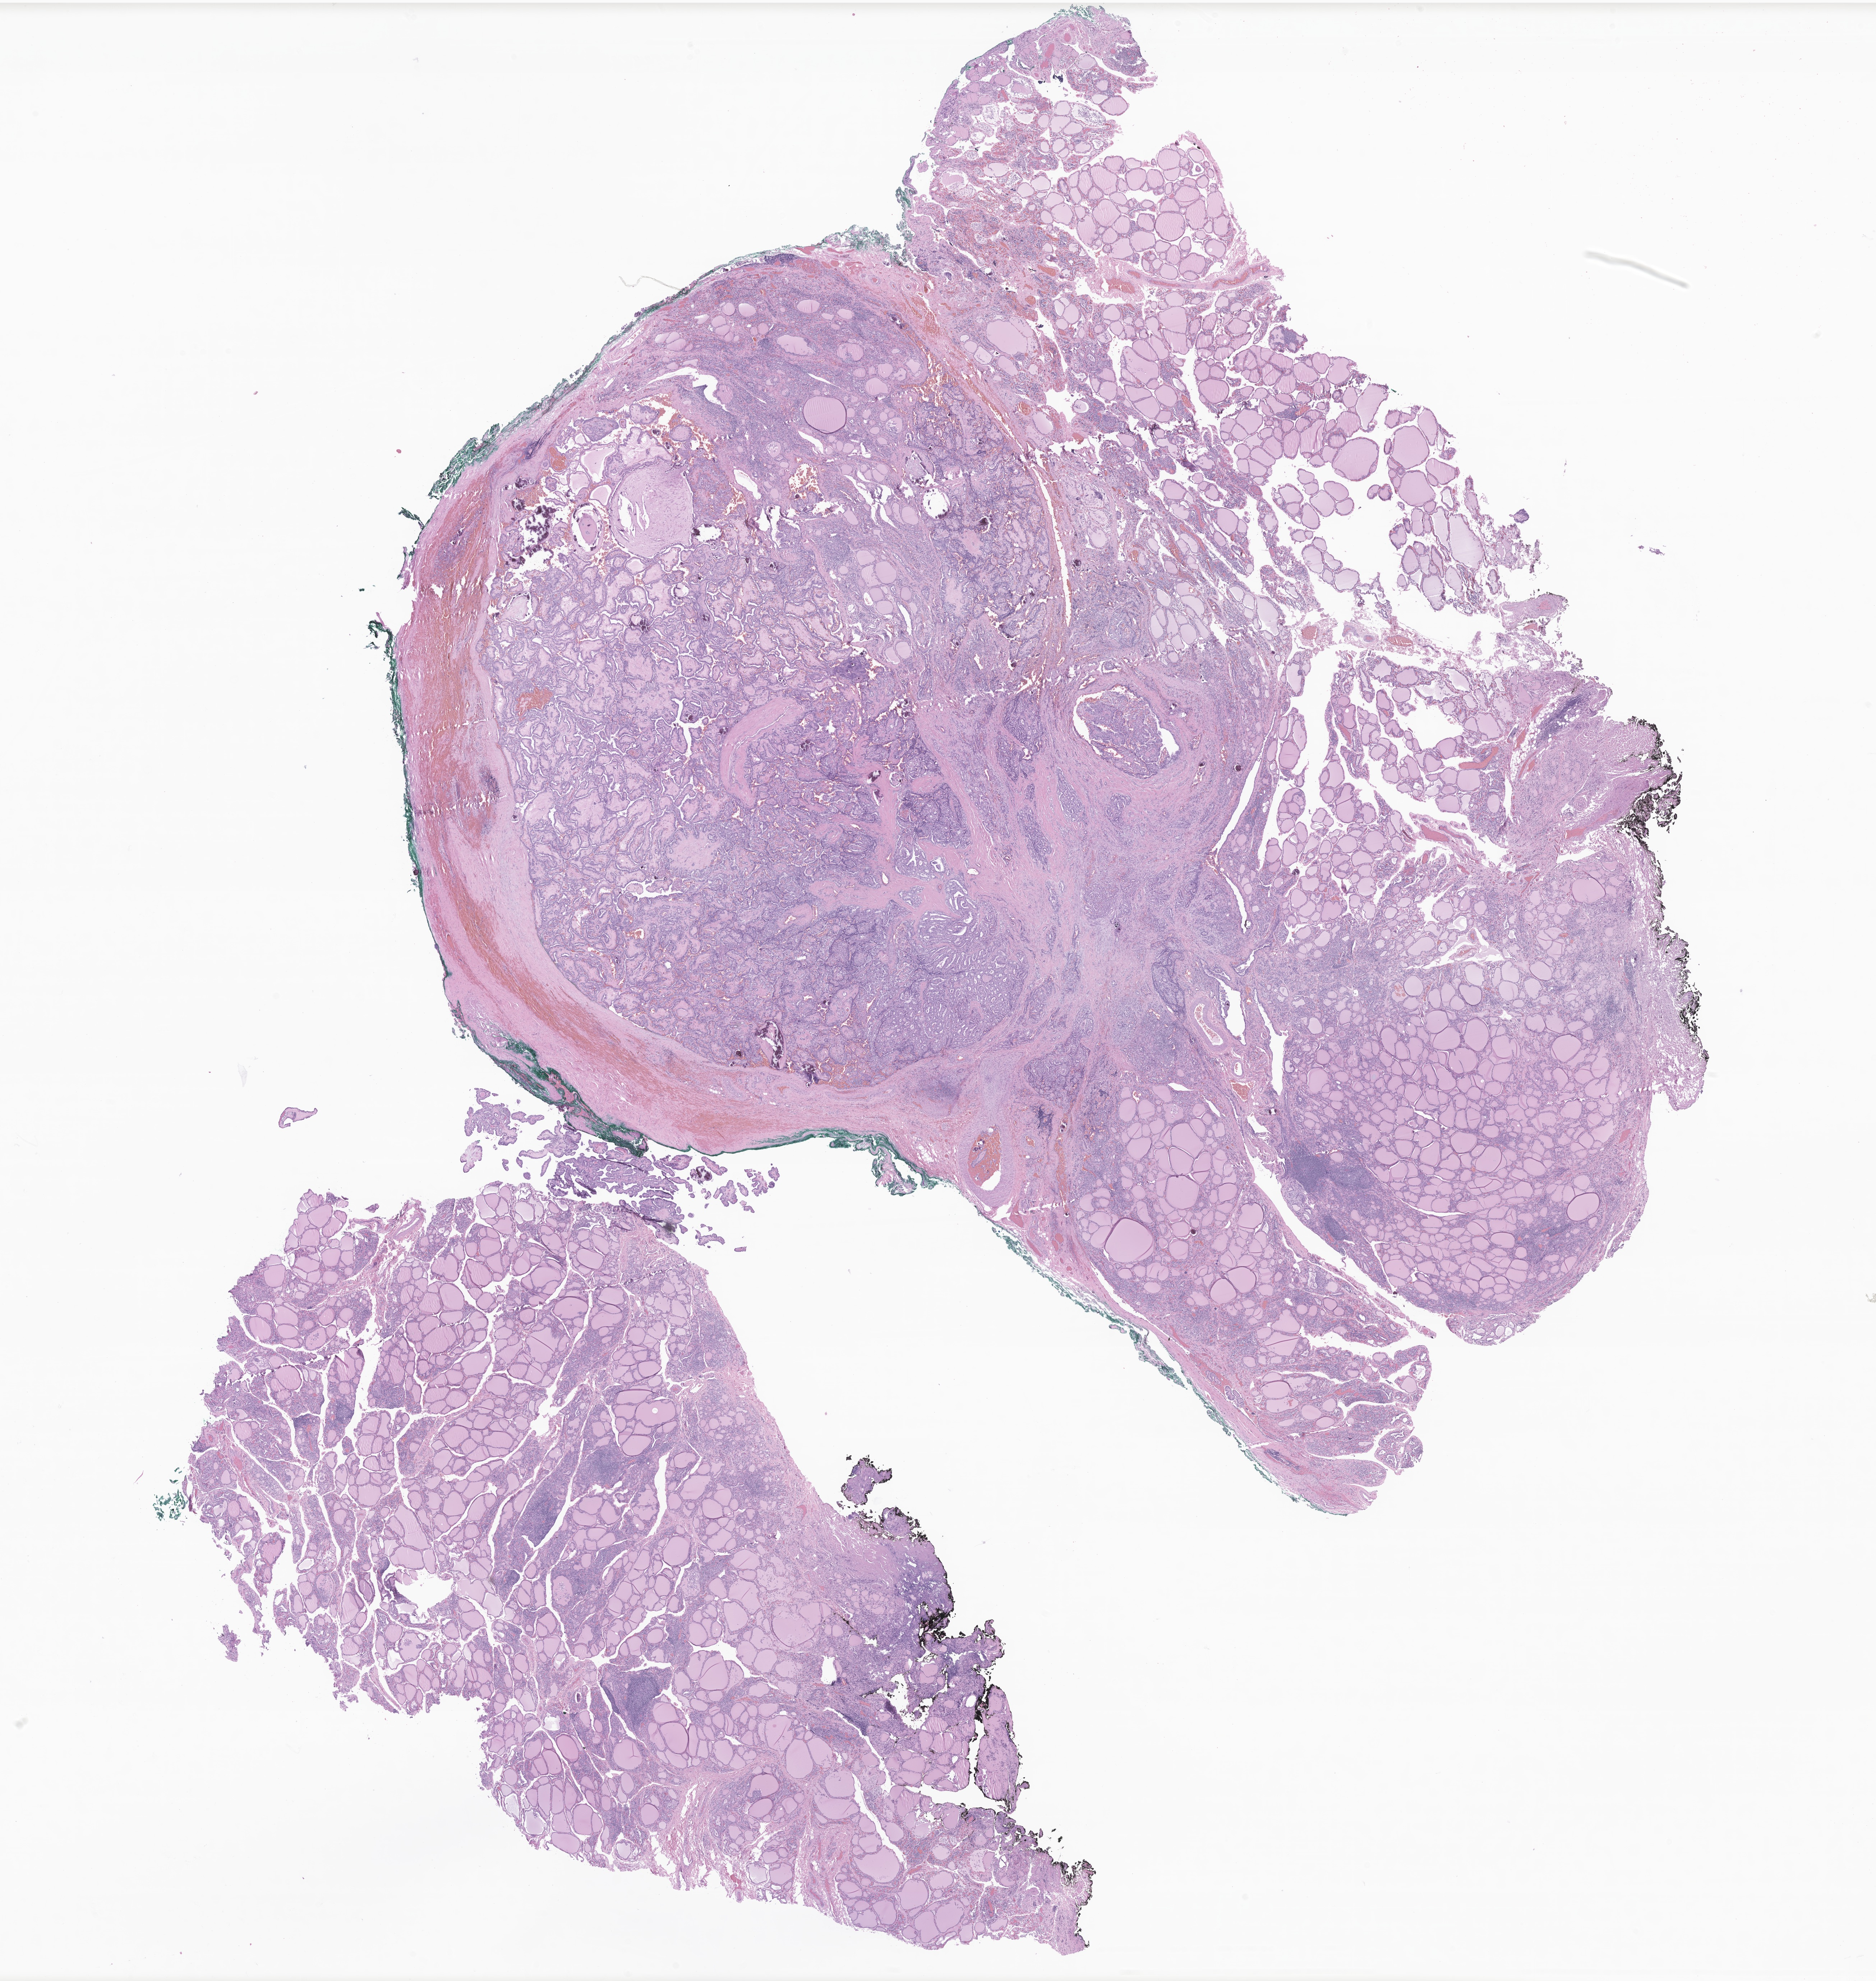
H&E whole-slide image of tumor tissue from the thyroid — shown as a low-resolution overview of the whole scanned area (about 22.0 x 23.2 mm). Formalin-fixed paraffin-embedded section. Female patient, age 223 months (18 years 7 months).
* diagnosis (ICD-O-3 morphology term): Papillary adenocarcinoma, NOS